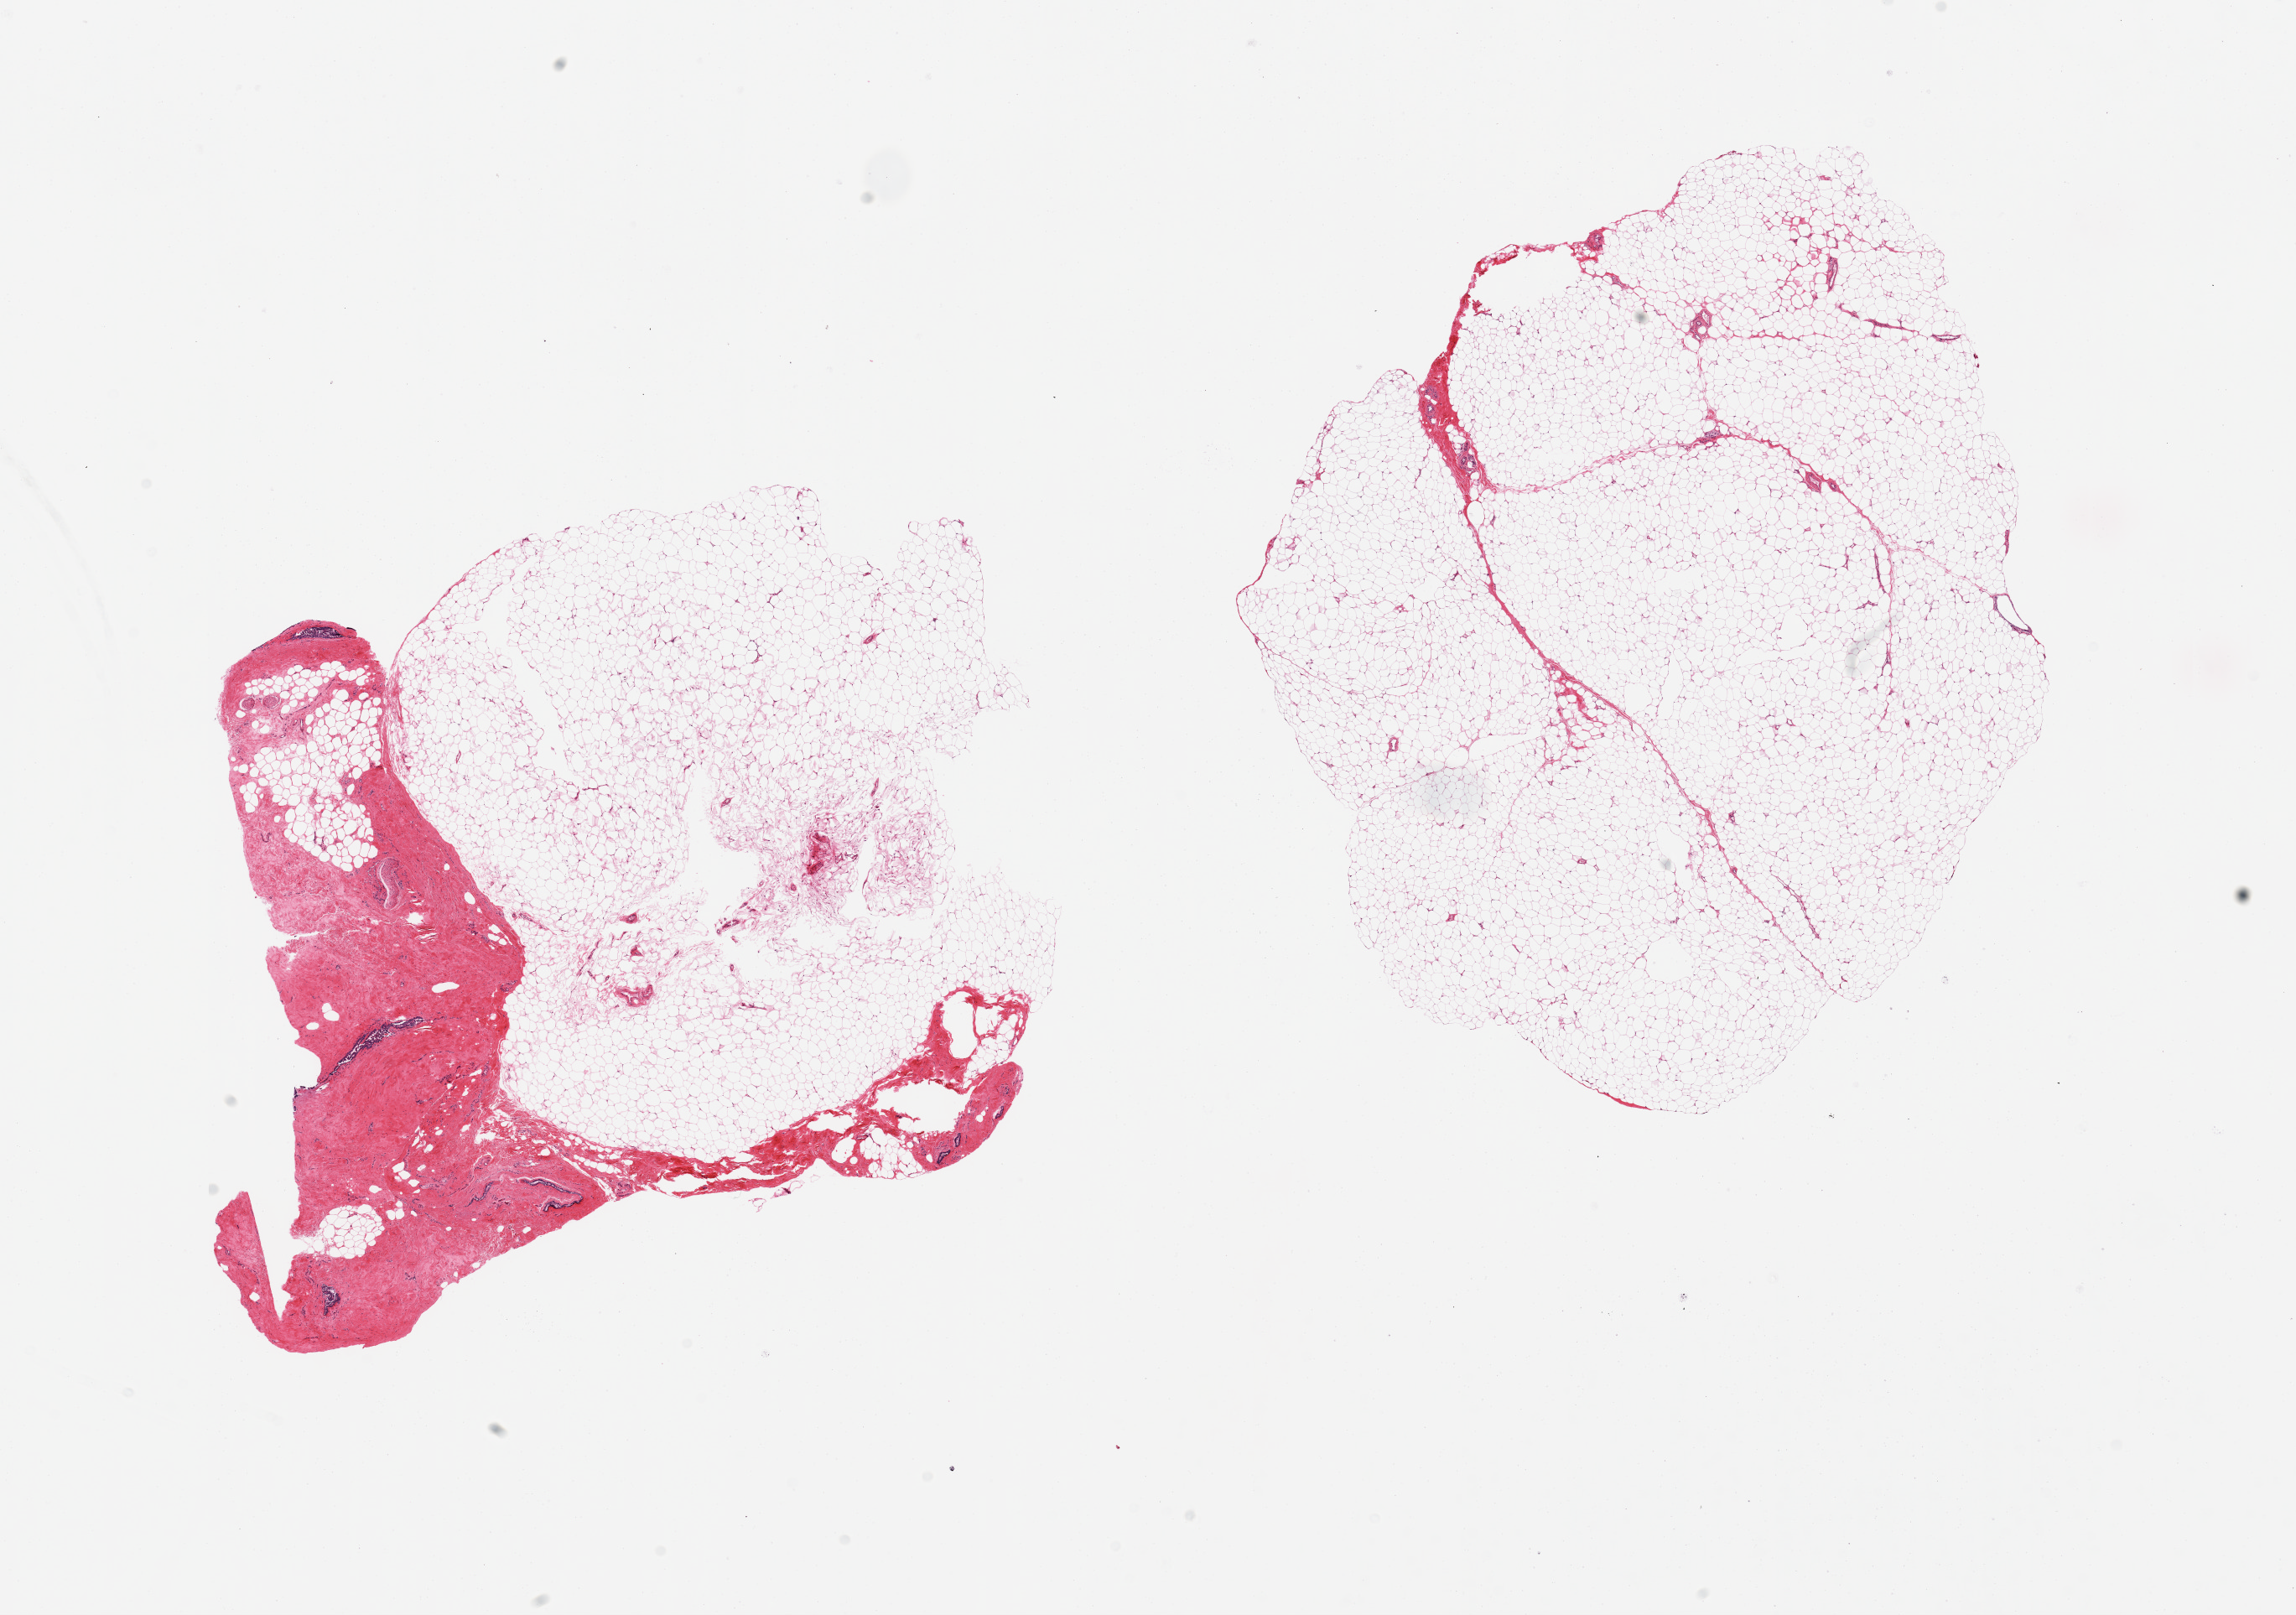
Digitized haematoxylin and eosin-stained section — whole scanned area (about 21.7 x 15.2 mm, acquisition: 20x scan) shown as a low-resolution overview, PAXgene-fixed paraffin-embedded (PFPE) section, target tissue: breast, donor tissue sample.
• review note (as recorded): 2 pieces, one entirely fat, second is predominantly fat with ~30% fibrous tissue with few ducts